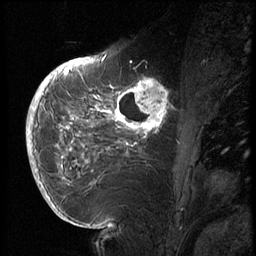
Breast MRI (dynamic contrast-enhanced), one sagittal slice; position 26 of 72 along the scan axis; 3 images stored at this slice position (order not interpretable as contrast timing); 1.5 T; TE 4.2 ms, TR 8.9 ms; 2.5 mm slice thickness; 256 × 256 image matrix, field of view 200 × 200 mm. Female patient, age 56 years. From the clinical record (not read from this slice): setting: breast cancer imaged before/during neoadjuvant chemotherapy.
Annotated regions visible in this slice (semi-automatic segmentation, software-assisted and operator-edited):
- analysis volume of interest (the breast-tissue region the enhancement analysis was run in; not a lesion): bounding box [x1, y1, x2, y2] px = [114, 76, 177, 138]
- tumour enhancement mask (voxels above the 140 % enhancement threshold inside the analysis volume of interest): [114, 78, 170, 134]